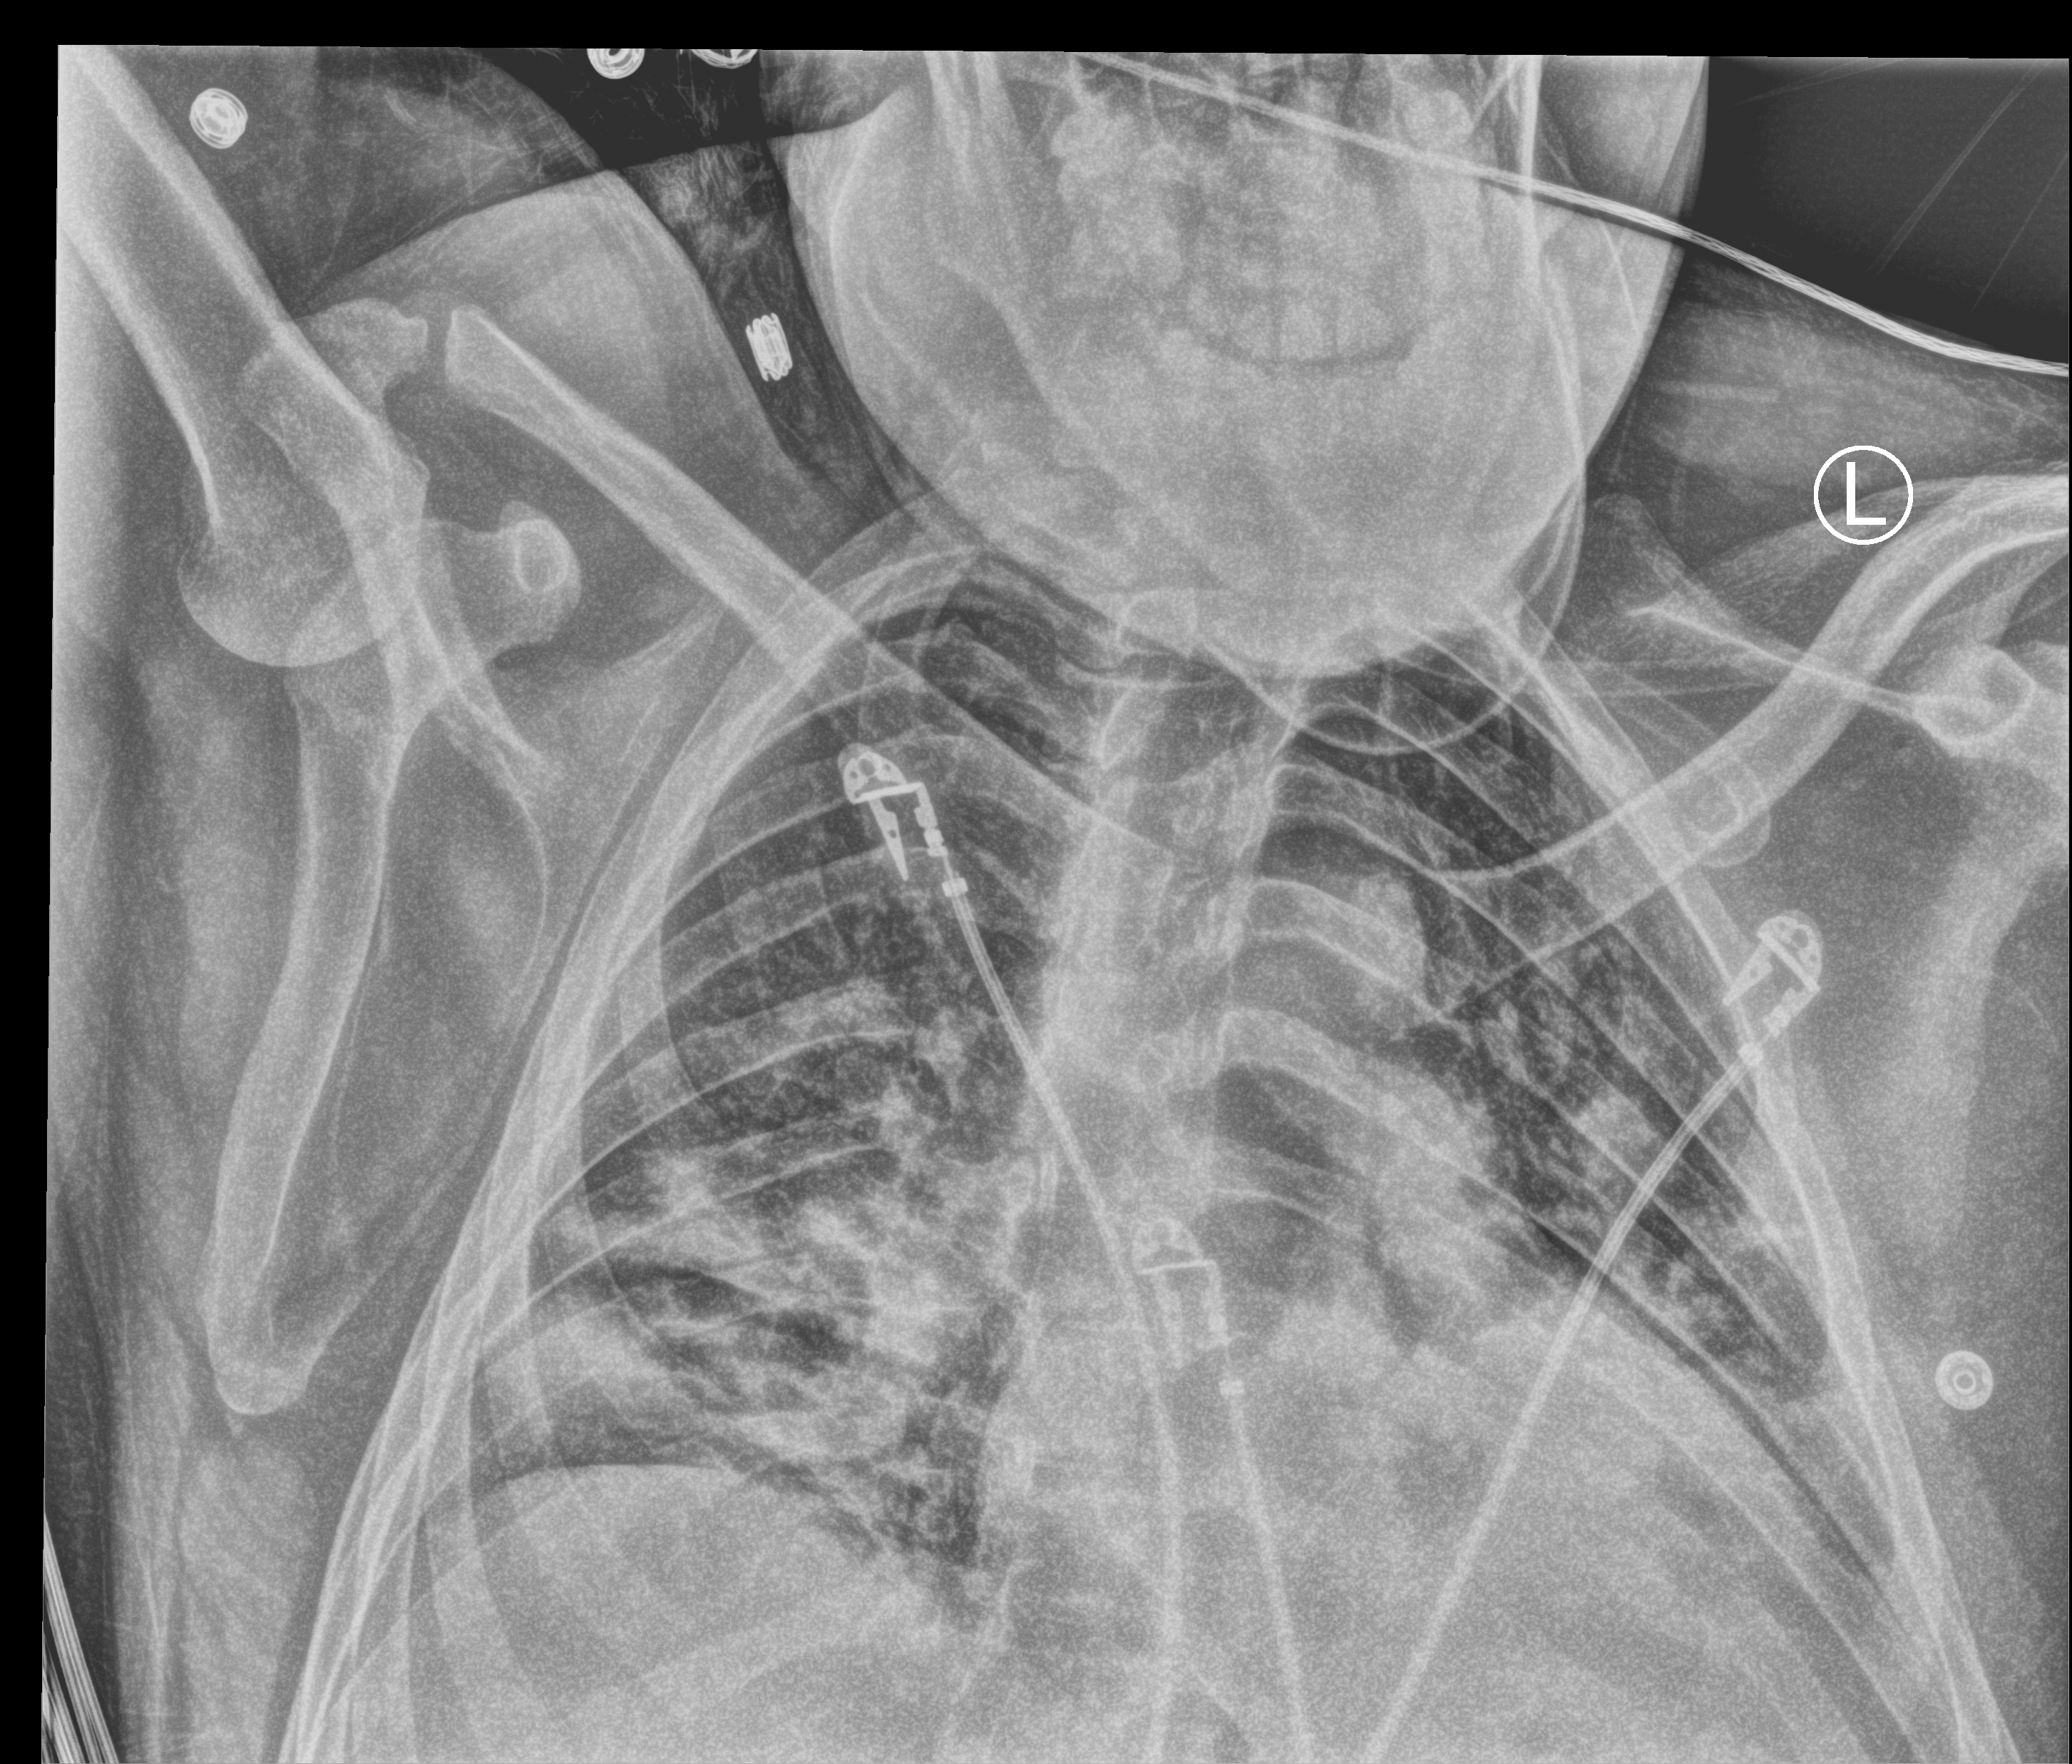
Bedside chest radiograph (computed radiography), anteroposterior (AP) projection. Patient hospitalised with COVID-19; male, aged 18–59 years.
Admission-level facts for this patient (not findings on this image; timing relative to this image not recorded):
- admitted to intensive care during this hospital stay: no
- length of hospital stay: 9 days